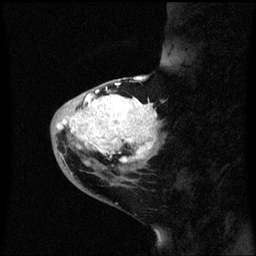
Breast MRI (dynamic contrast-enhanced), one sagittal slice. Position 20 of 60 along the scan axis. Dynamic contrast-enhanced series, image 2 of 3 at this slice position (ordered by acquisition). 1.5 T. TE 4.2 ms, TR 8.4 ms. 256 × 256 image matrix. Female patient, age 46 years. Case-level facts recorded for this patient, not image findings: setting: breast cancer imaged before/during neoadjuvant chemotherapy; receptor status: HER2-positive.
Outlined on this slice (semi-automatically segmented with operator editing):
- analysis volume of interest (the breast-tissue region the enhancement analysis was run in; not a lesion): bounding box <50,86,165,171> (left, top, right, bottom; pixels)
- tumour enhancement mask (voxels above the 70 % enhancement threshold inside the analysis volume of interest): <58,90,159,163>